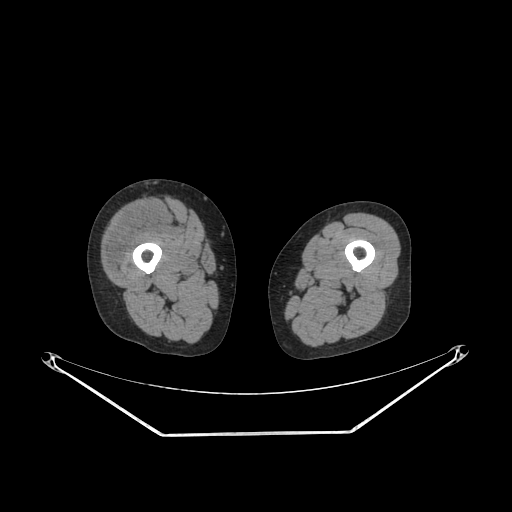
CT of an extremity soft-tissue mass (from a PET/CT study), one axial slice; position 222 of 311 along the scan axis; reconstruction kernel SOFT; soft-tissue window (W 400 / L 40 HU); 512 × 512 image matrix, field of view 500 × 500 mm. Female patient. From the clinical record (not read from this slice): histological type: pleiomorphic undifferentiated sarcoma; grade: high; site of the primary tumour: right quadricep.
Structures marked on this image (expert contour drawn on MRI and transferred to this co-registered scan by the dataset authors):
- tumour plus oedema (research contour): bounding box (x1, y1, x2, y2) in pixels: (107, 203, 163, 273)